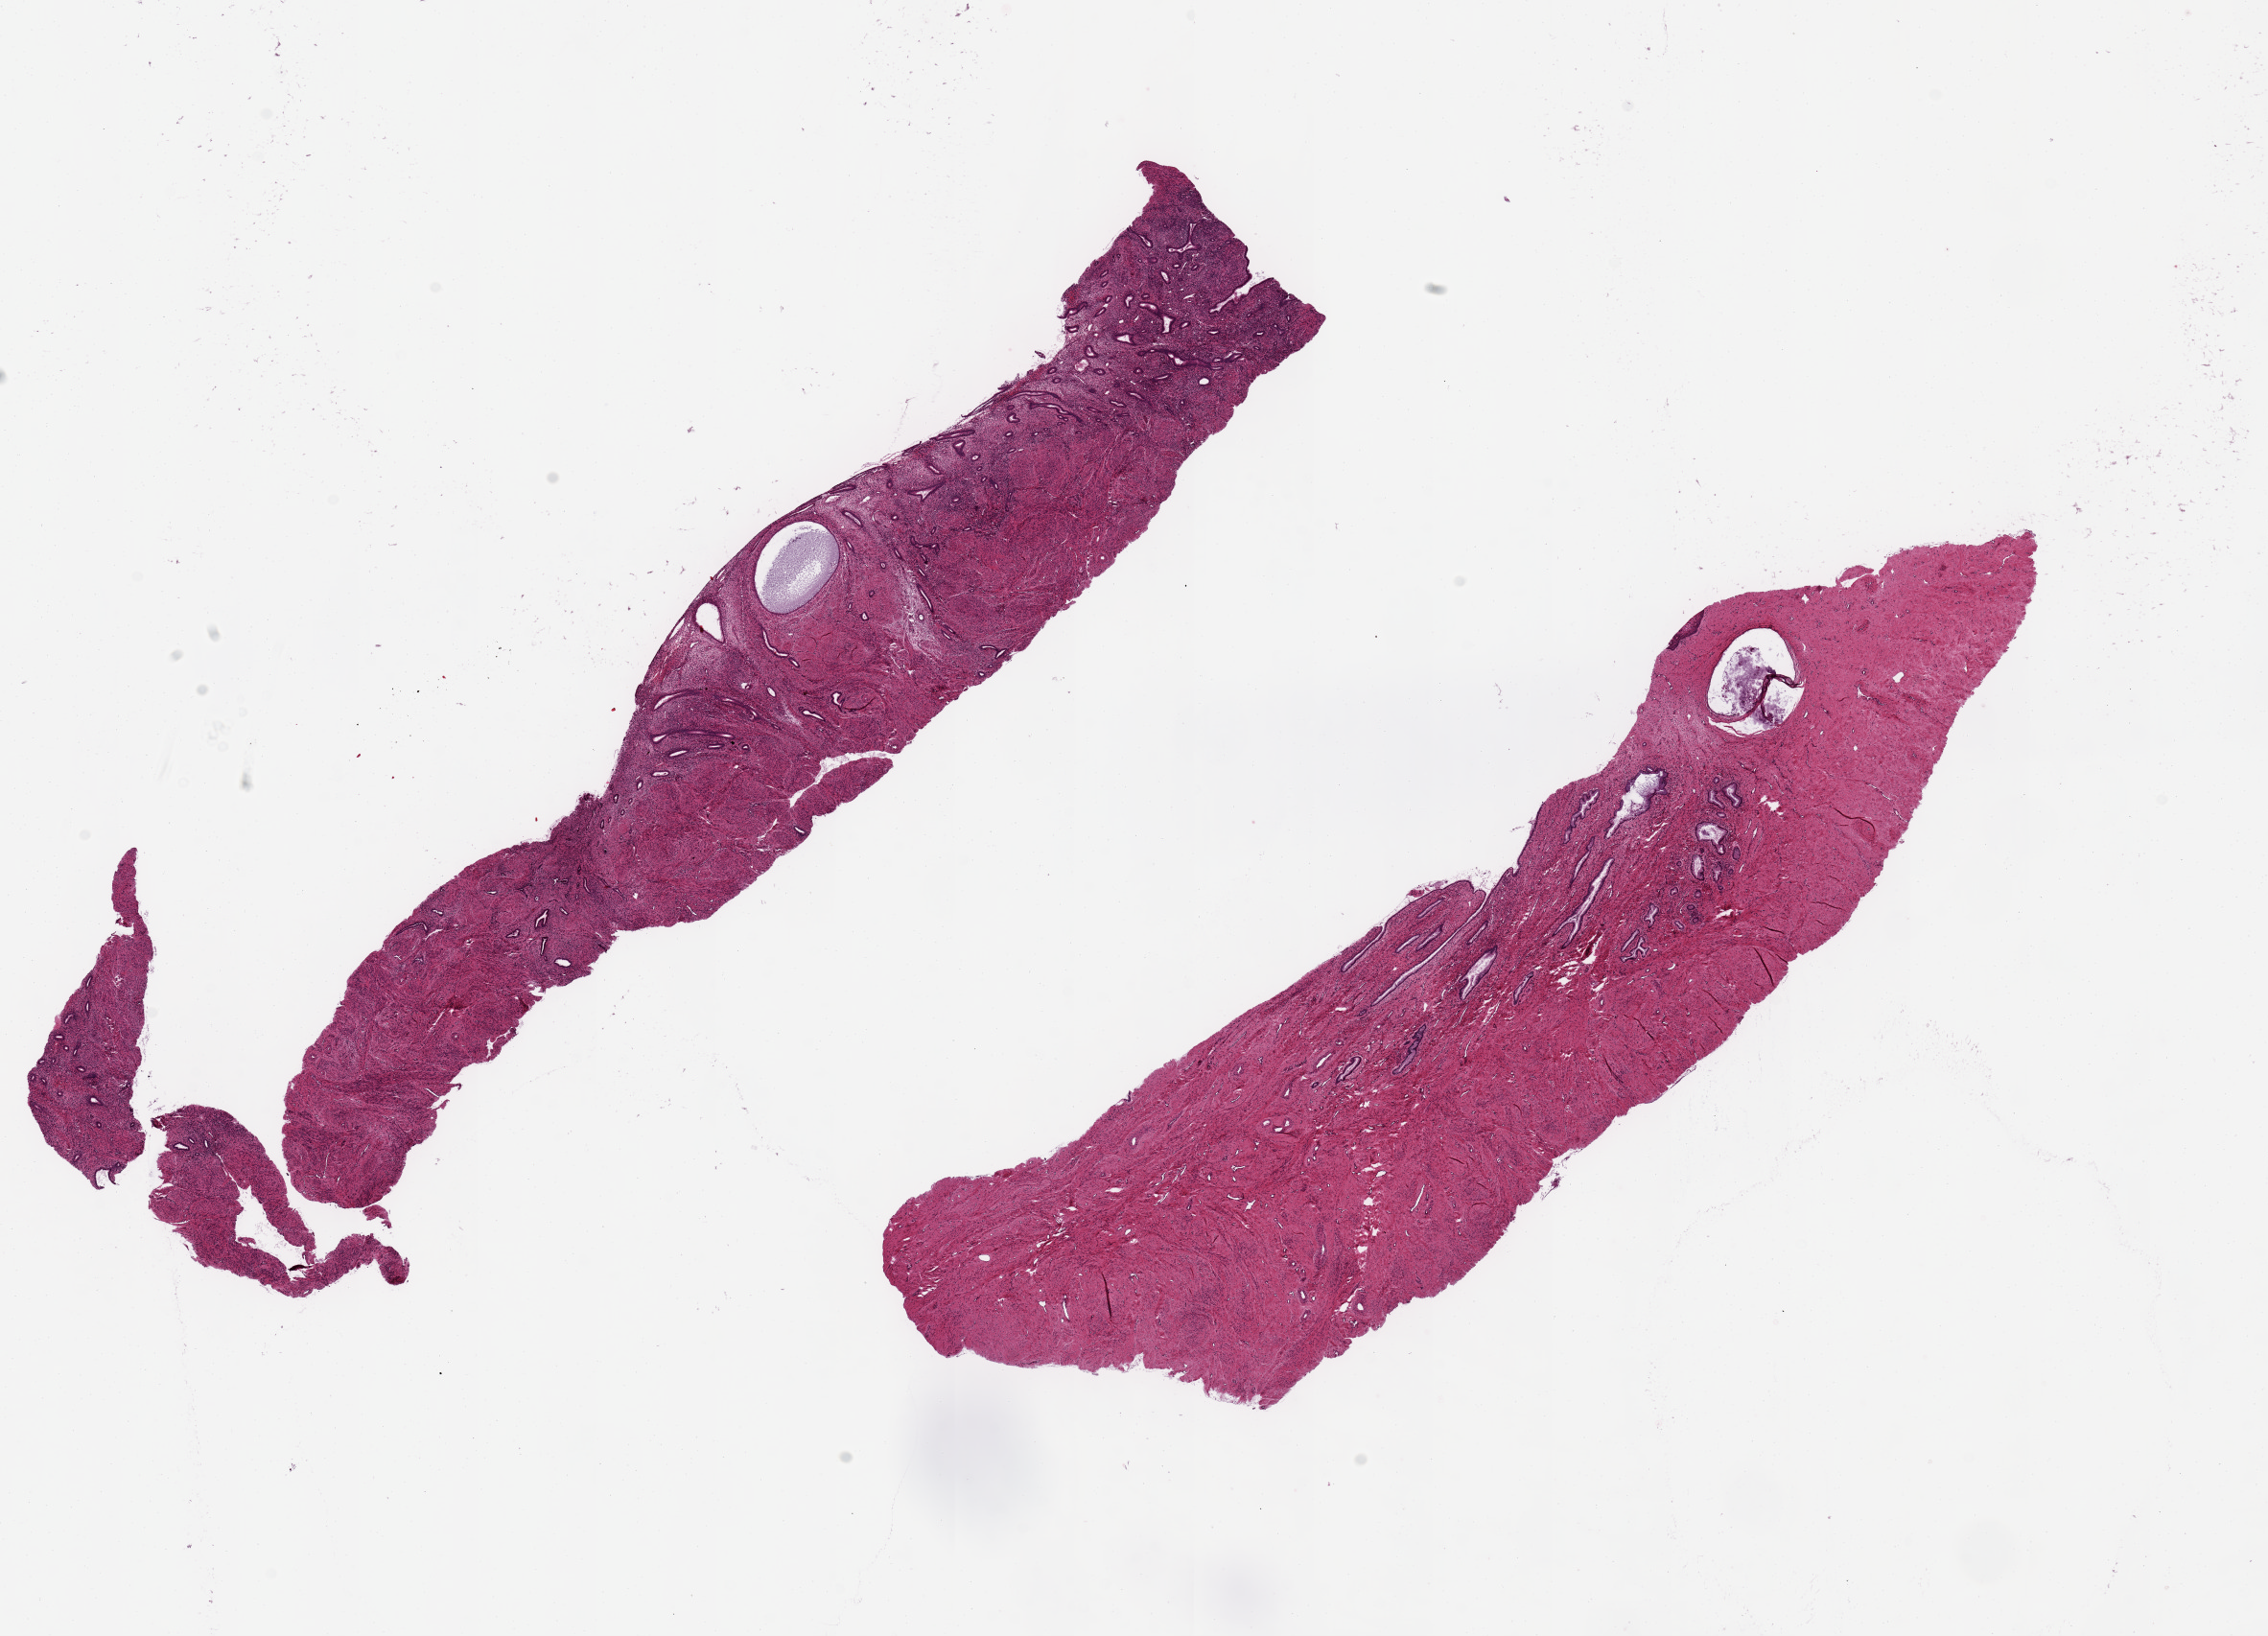
Digitized H&E-stained section, a low-resolution overview of the entire scanned area, about 18.7 x 13.5 mm (from a 20x scan). PAXgene-fixed paraffin-embedded (PFPE) section. Target tissue: endocervix. Donor tissue sample. Donor sex: female.
• pathologist's review note for this sample: 2 ~10.5x2.2mm aliquots, each ~40 glandular tissue. One aliquot is more upper endo-cervix/lower uterine segment